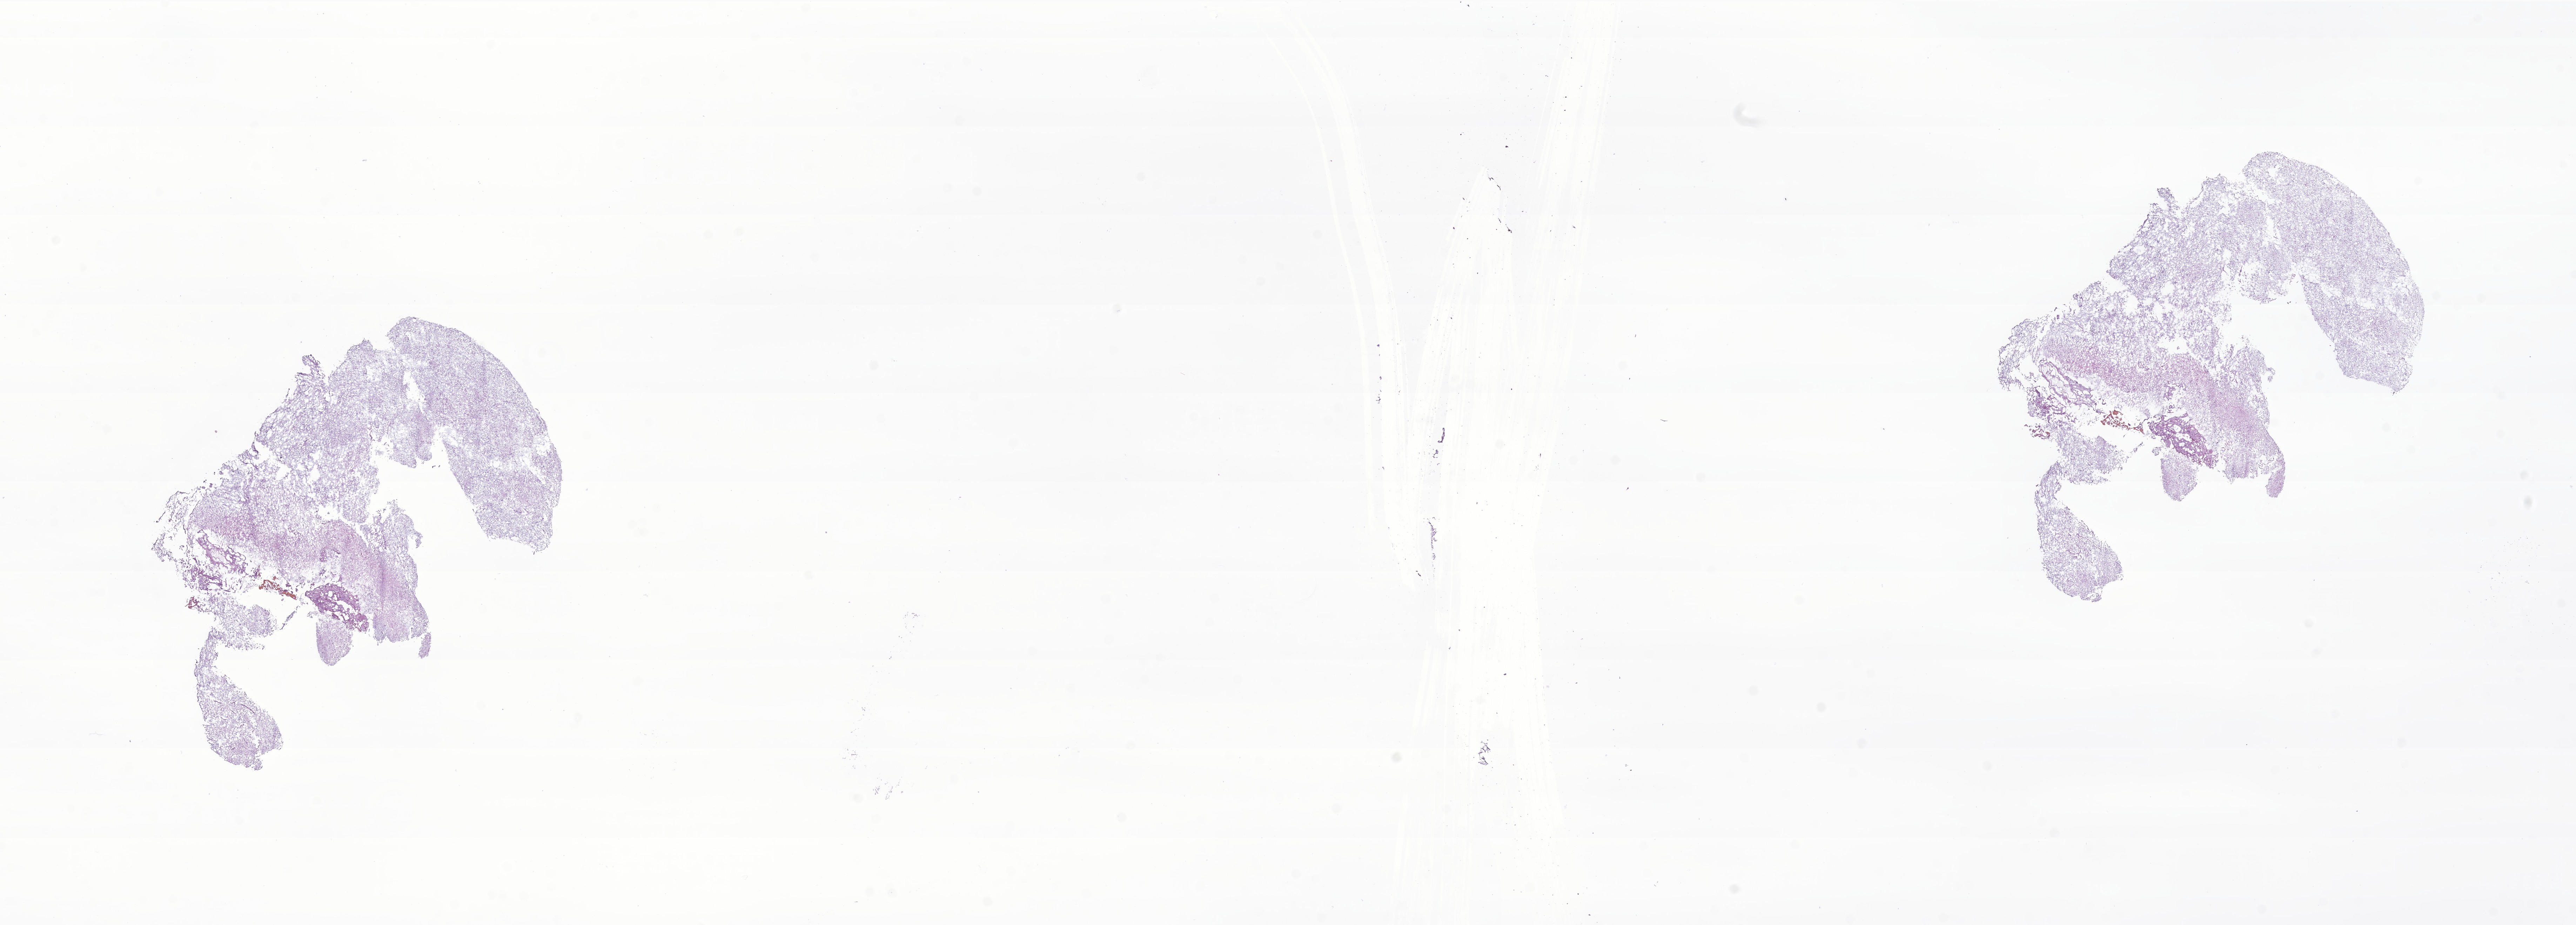
Whole-slide image, H&E stain of tumor tissue from the brain, a low-resolution overview of the entire scanned area, about 31.0 x 11.1 mm; frozen section. Patient: female, age 109 months (9 years 1 month).
• recorded diagnosis: Pilocytic astrocytoma